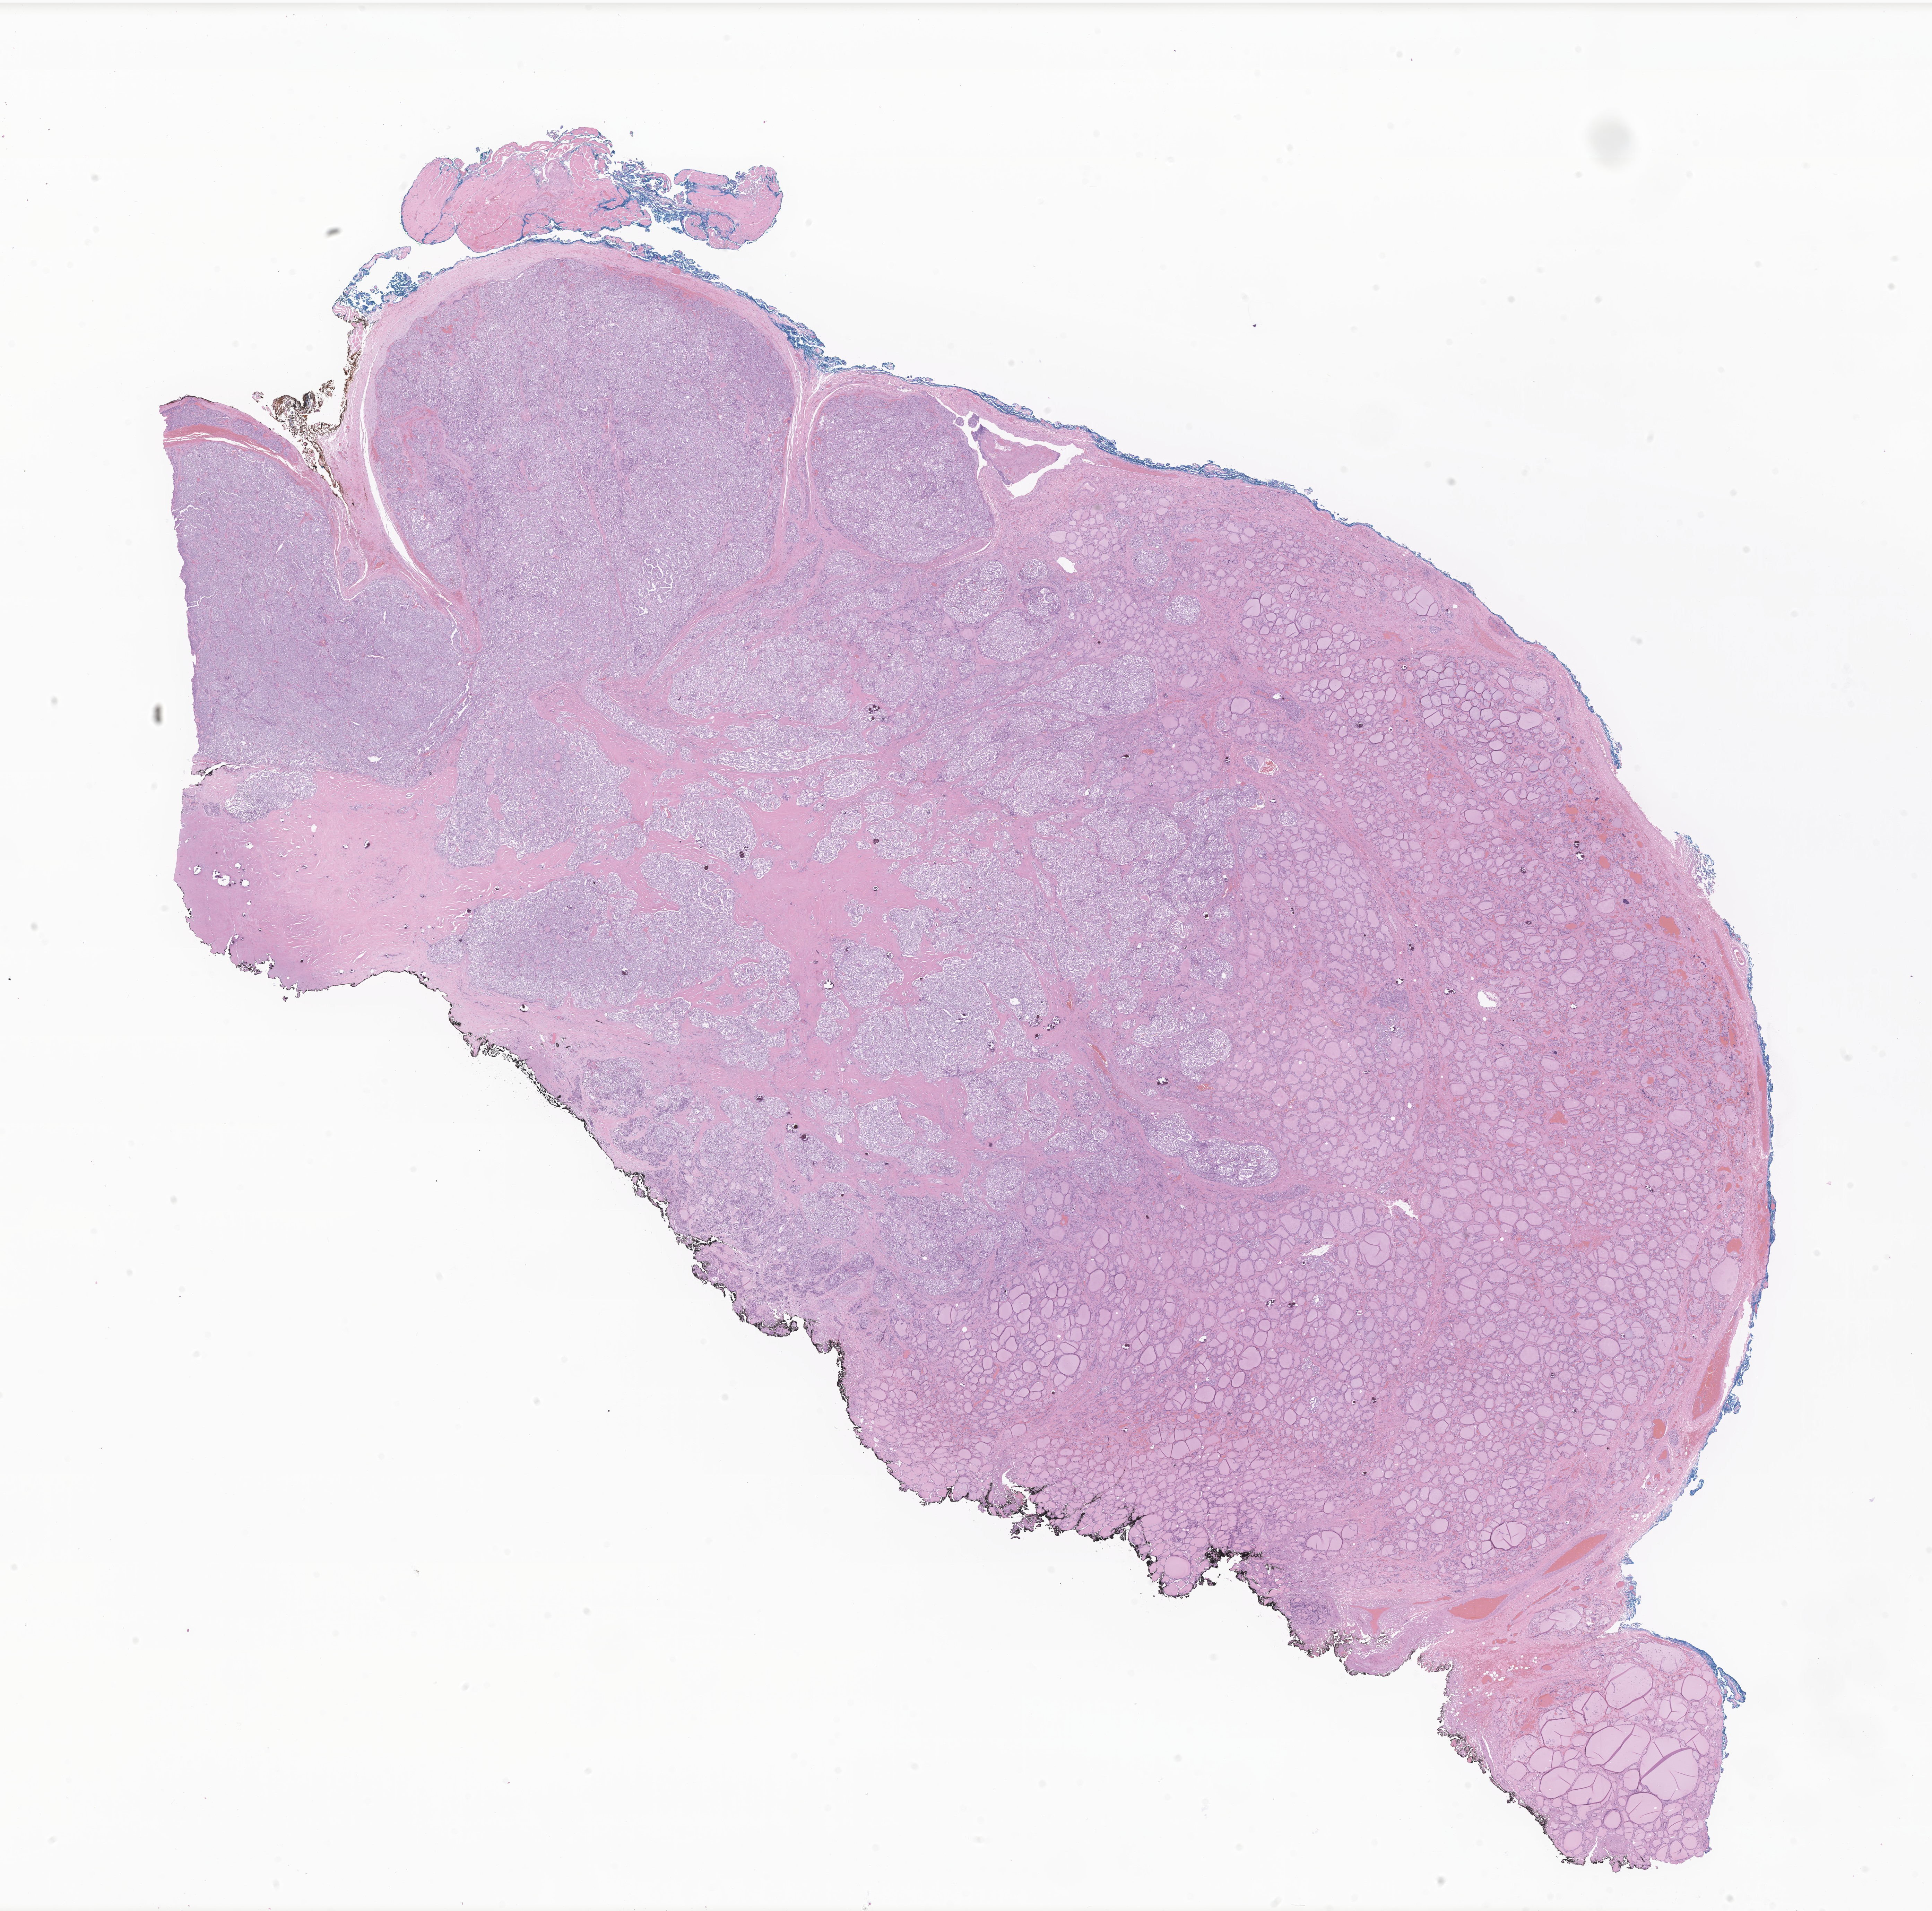
Digitized hematoxylin and eosin (H&E)-stained section of tumor tissue from the thyroid — low-resolution overview of the scanned area, about 23.5 x 23.2 mm, formalin-fixed paraffin-embedded section. Patient female; age 179 months (14 years 11 months).
Diagnosis (ICD-O-3 morphology term): Carcinoma, metastatic, NOS.